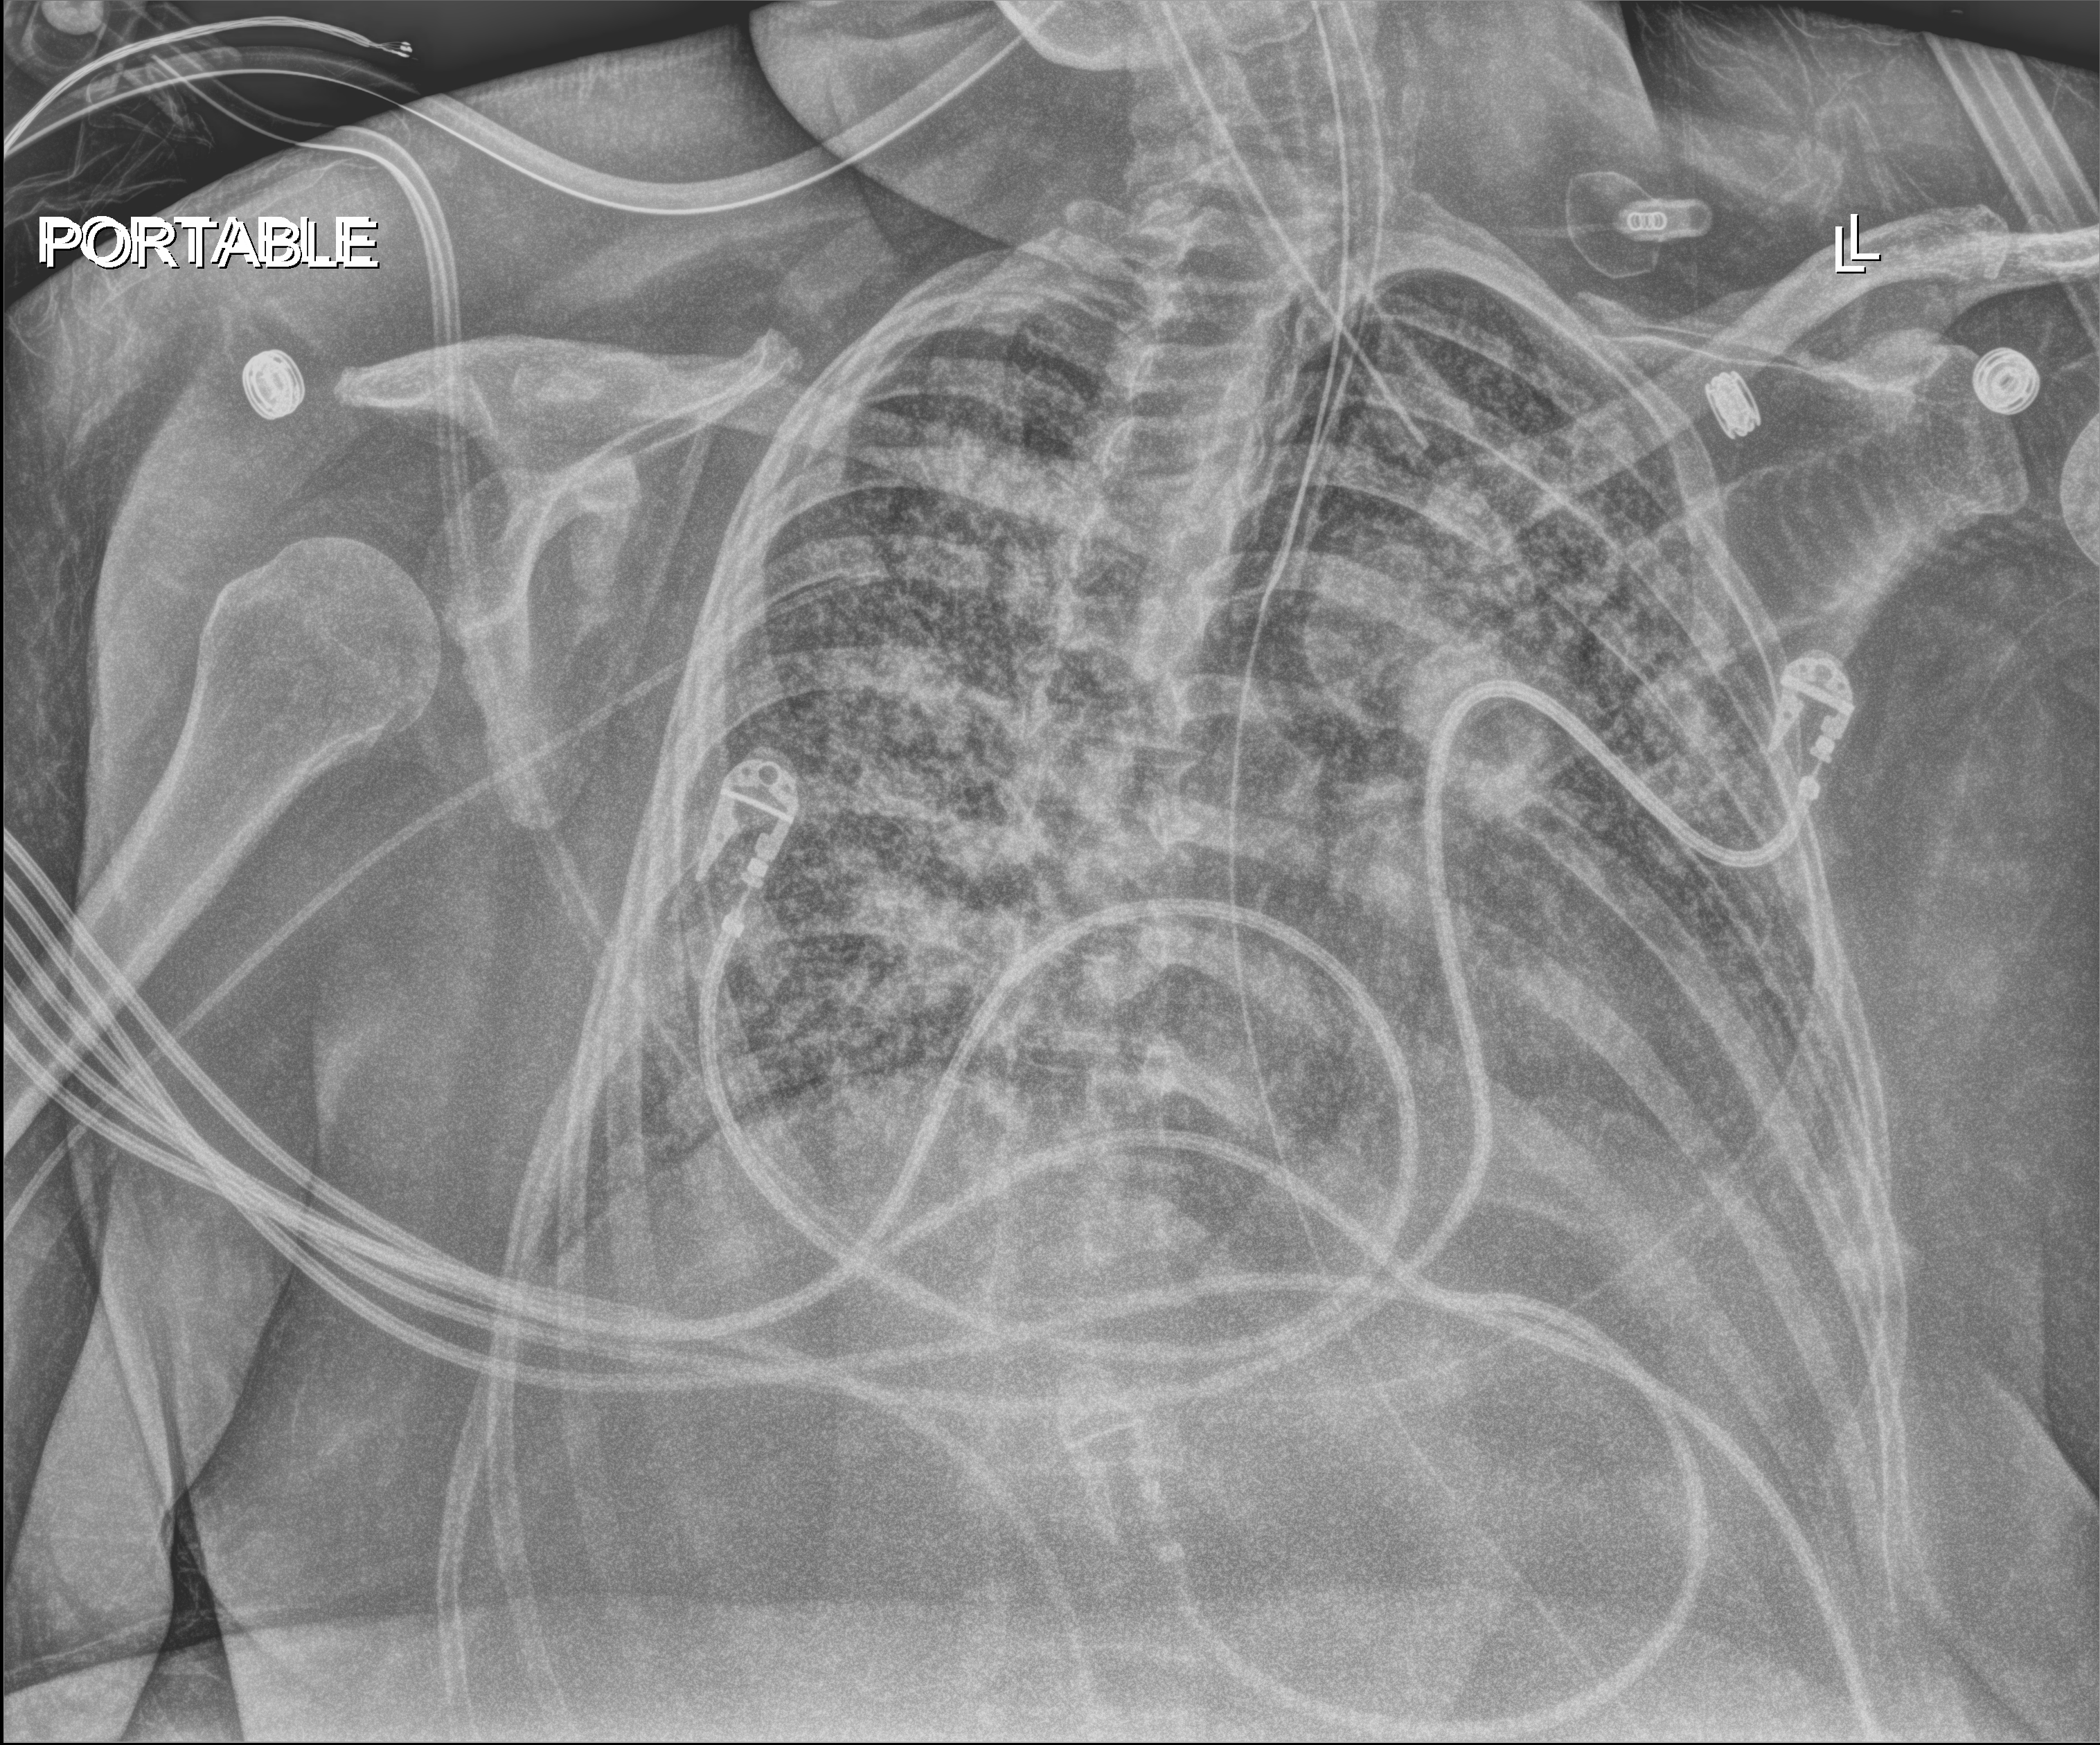
Chest X-ray (portable); anteroposterior (AP) projection. Patient hospitalised with COVID-19; female, aged 18–59 years.
From the hospital-stay record, not from the radiograph (when in the stay this image was taken is not recorded): mechanically ventilated during this hospital stay: yes; admitted to intensive care during this hospital stay: yes.